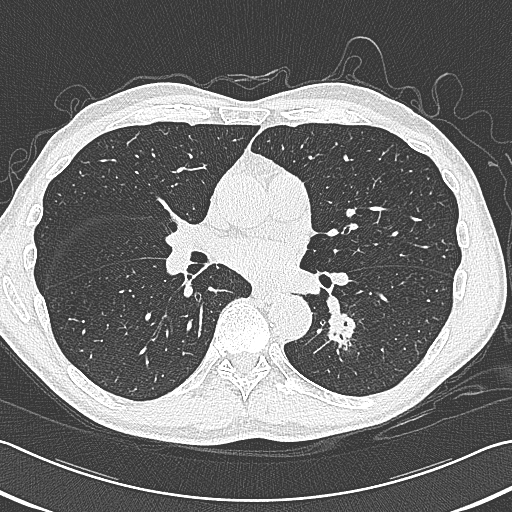
Chest CT (low-dose screening protocol), one axial image, baseline screening round, lung window (W 1500 / L -600 HU), 1 mm slice thickness, lung (sharp) reconstruction kernel (B80f), slice 173 of 354 in the series, 512 × 512 image matrix, field of view 346 × 346 mm. Male, age 59 years at enrolment.
Expert reader's lesion annotation, bounding box (x1, y1, x2, y2) in pixels: (313, 294, 376, 353). Reader record for this screening exam (exam-level; its link to the box is not recorded): non-calcified nodule or mass ≥4 mm, left lower lobe, 15 × 15 mm, smooth margins, soft tissue attenuation. Lung cancer was diagnosed 17 days after this screen: squamous cell carcinoma, large cell, nonkeratinizing, NOS, left lower lobe, poorly differentiated (G3), stage IB (AJCC 6th edition), 31 mm at pathology.